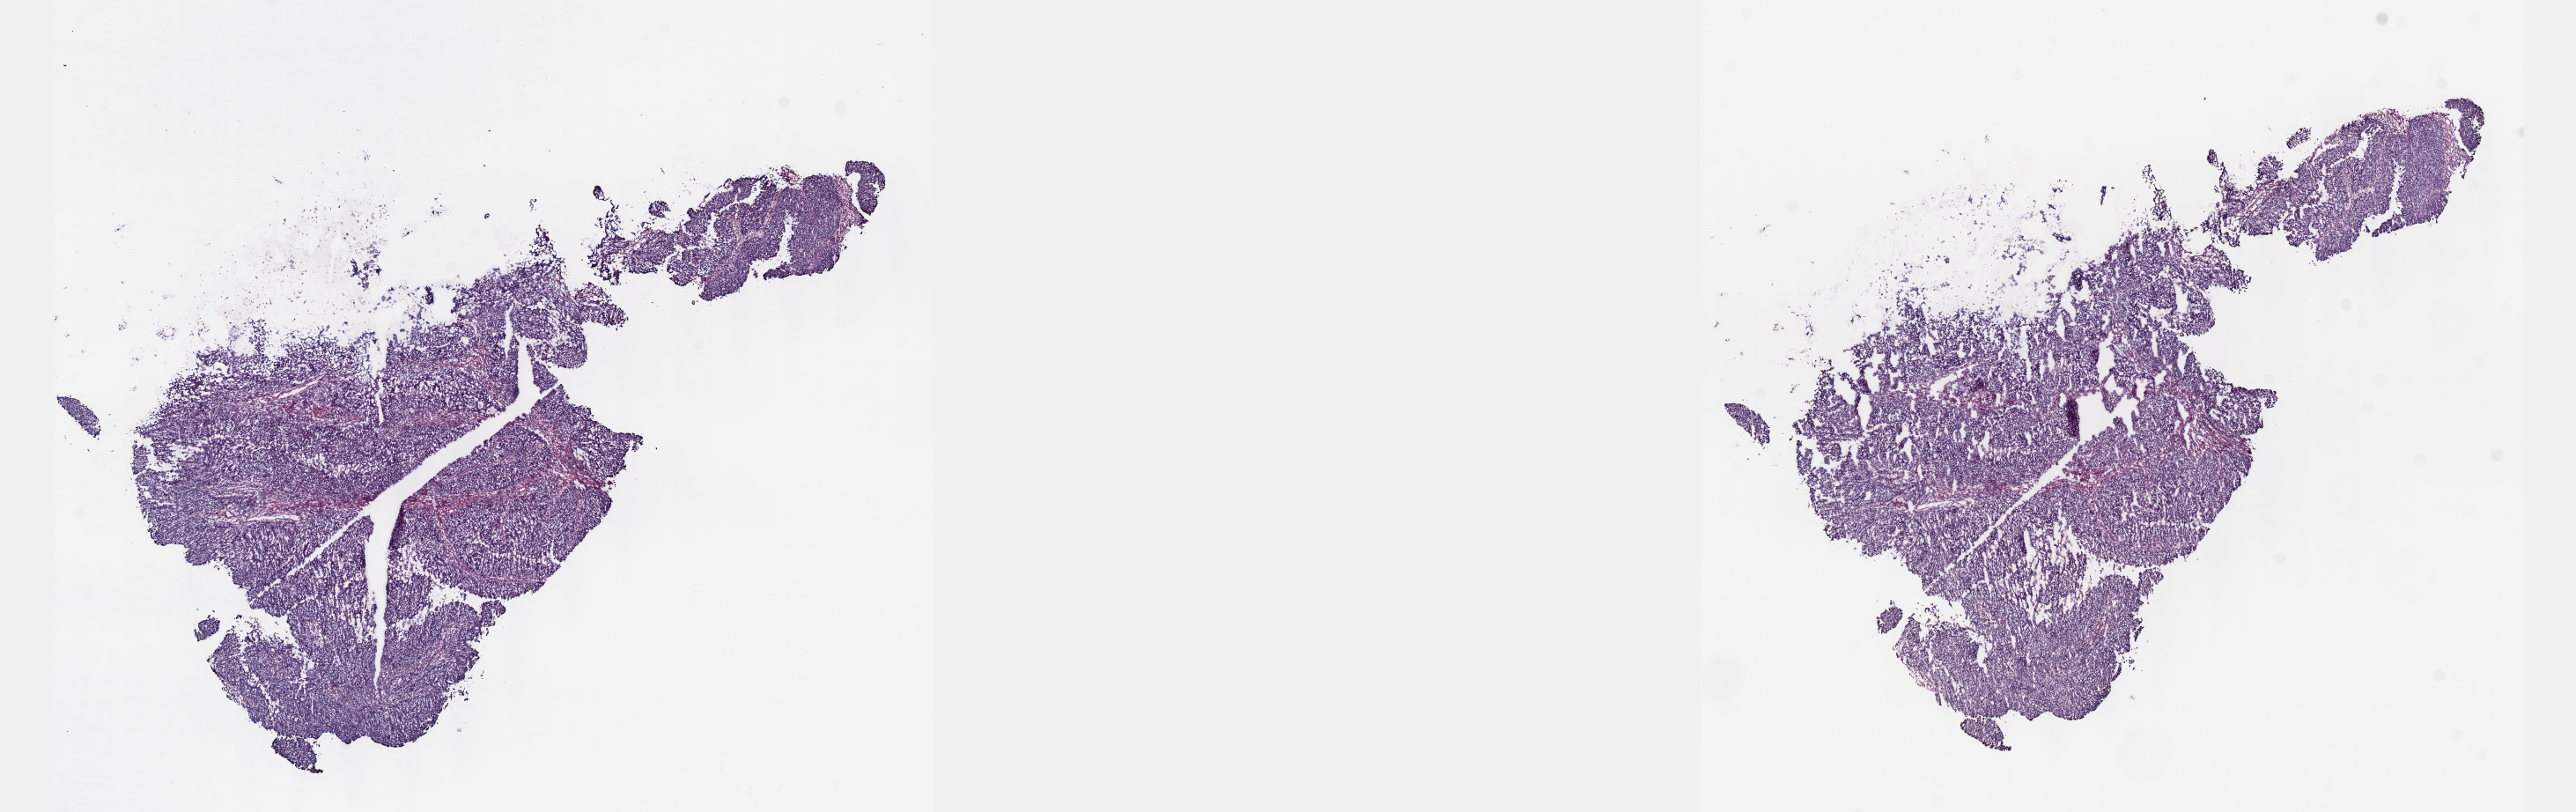
Whole-slide histology image, Hematoxylin and eosin (H&E) stained — a low-resolution overview of the entire scanned area, about 23.6 x 7.5 mm; frozen section from the top of the tissue portion; bladder, primary tumour sample. Male, age 75 years at initial diagnosis. Histologic grade: high grade. Composition of this section per pathologist review: tumour cells 80%, tumour nuclei 90%, normal cells 0%, stromal cells 20%, necrosis 0%. Infiltration values recorded for this section: lymphocyte infiltration 0%, monocyte infiltration 0%, neutrophil infiltration 0%.
AJCC pathologic stage: II (6th edition). Diagnosis: Papillary transitional cell carcinoma (lateral wall of bladder).